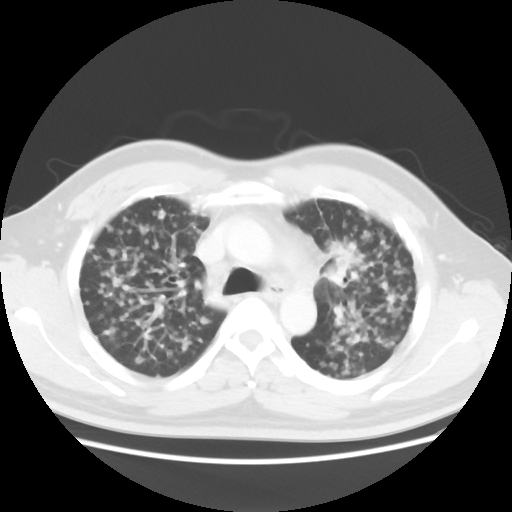
Chest CT, one axial slice; position 27 of 40 along the scan axis; reconstruction kernel STANDARD; lung window (W 1500 / L -600 HU); 512 × 512 image matrix, field of view 366 × 366 mm. Patient: male, 41 years. From the clinical record (not read from this slice): clinical TNM (as recorded): T1c N3 M1b; histopathological grade: G2-3.
Annotated regions visible in this slice (rectangle marked by the reading radiologist):
- lung tumour (recorded histology: adenocarcinoma): box from (x=323, y=239) to (x=363, y=292) px